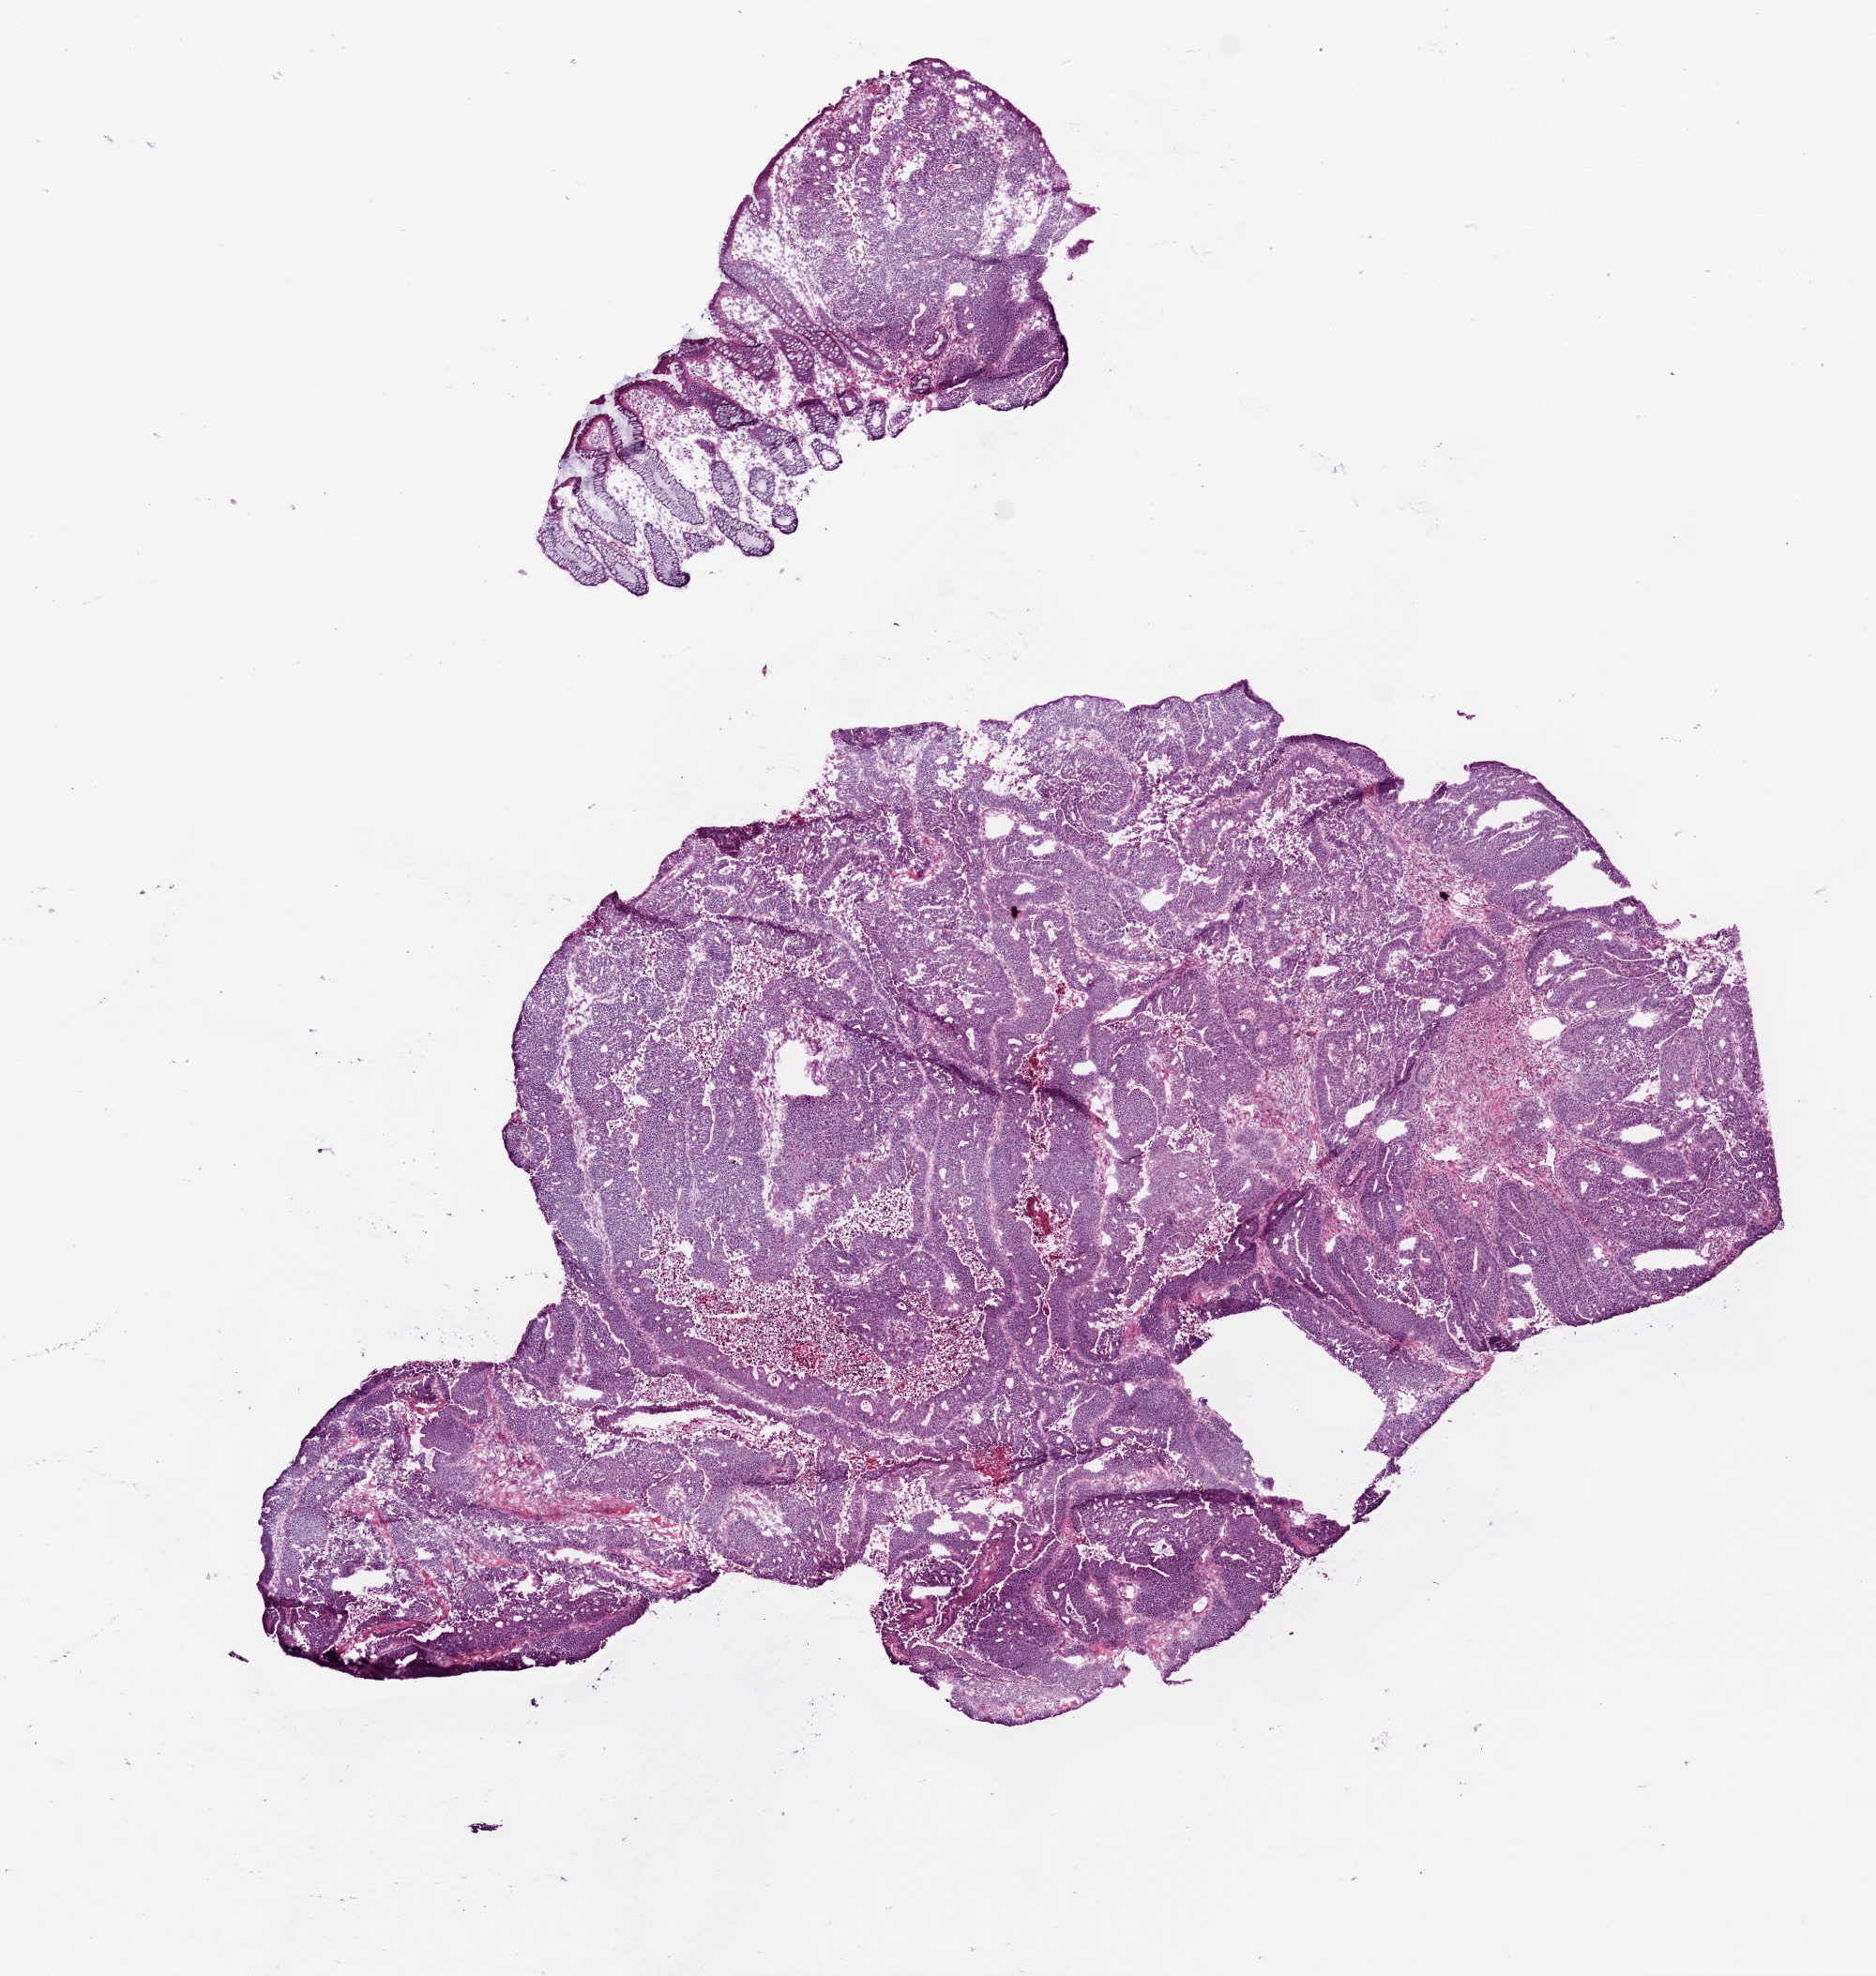
Whole-slide histology image, H&E-stained, shown as a low-resolution overview of the whole scanned area (about 8.0 x 8.5 mm, acquisition: 20x scan), frozen section from the bottom of the tissue portion, primary tumour sample from the colon. Male, age 84 years at initial diagnosis. Pathologist review of this section (percent, as recorded): tumour cells 90%, tumour nuclei 85%, normal cells 2%, stromal cells 0%, necrosis 8%. Infiltration values recorded for this section: lymphocyte infiltration 5%, neutrophil infiltration 1%.
AJCC pathologic stage: IIA (6th edition). Histologic diagnosis: Adenocarcinoma, NOS (sigmoid colon).